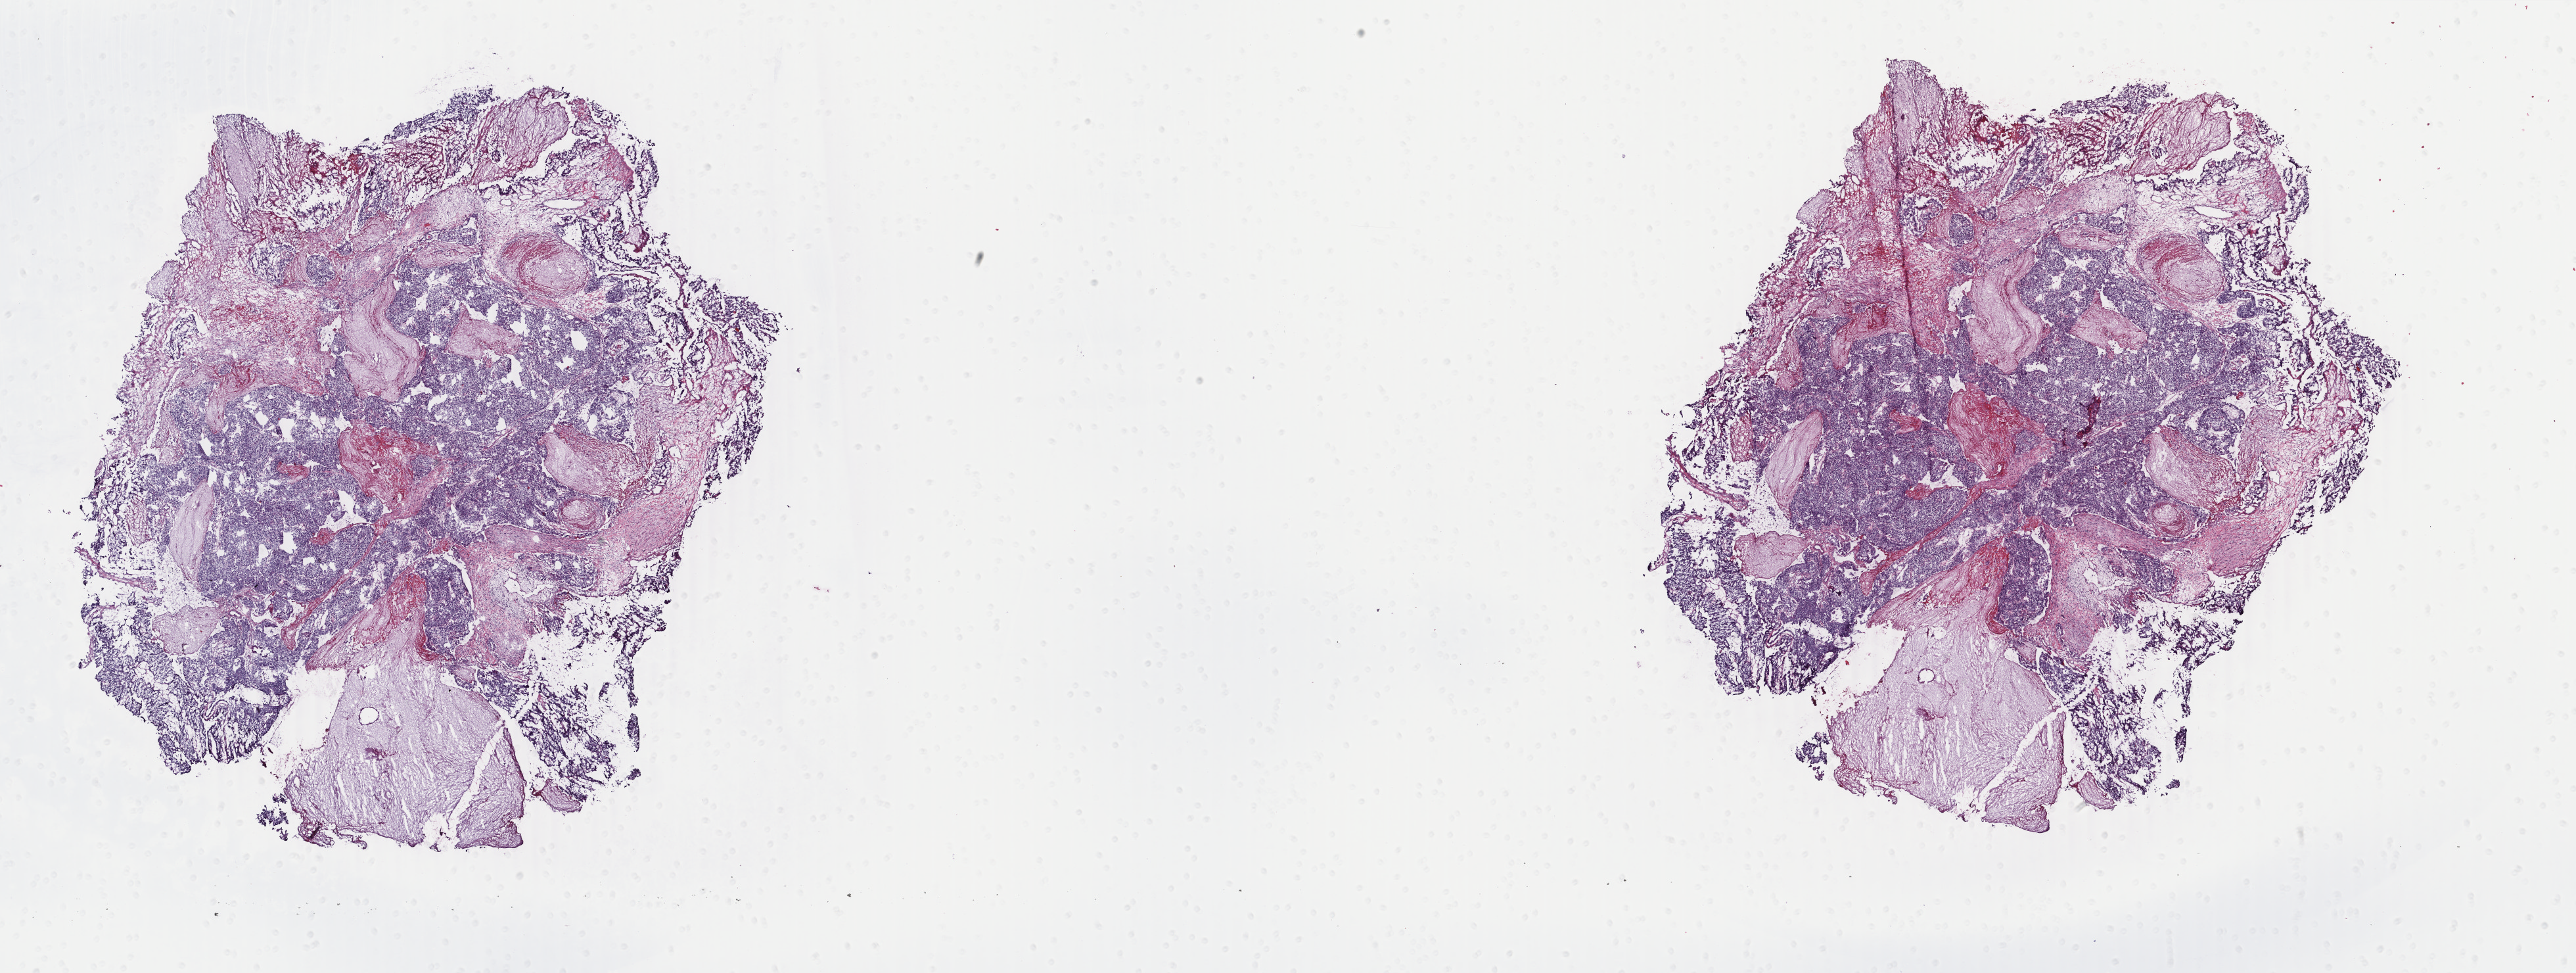
Digitized H&E tissue section (whole slide), low-resolution overview of the scanned area, about 31.2 x 11.8 mm; frozen section; bladder, primary tumour sample. Patient: male, age at initial diagnosis 73 years.
Diagnosis: Transitional cell carcinoma (dome of bladder).